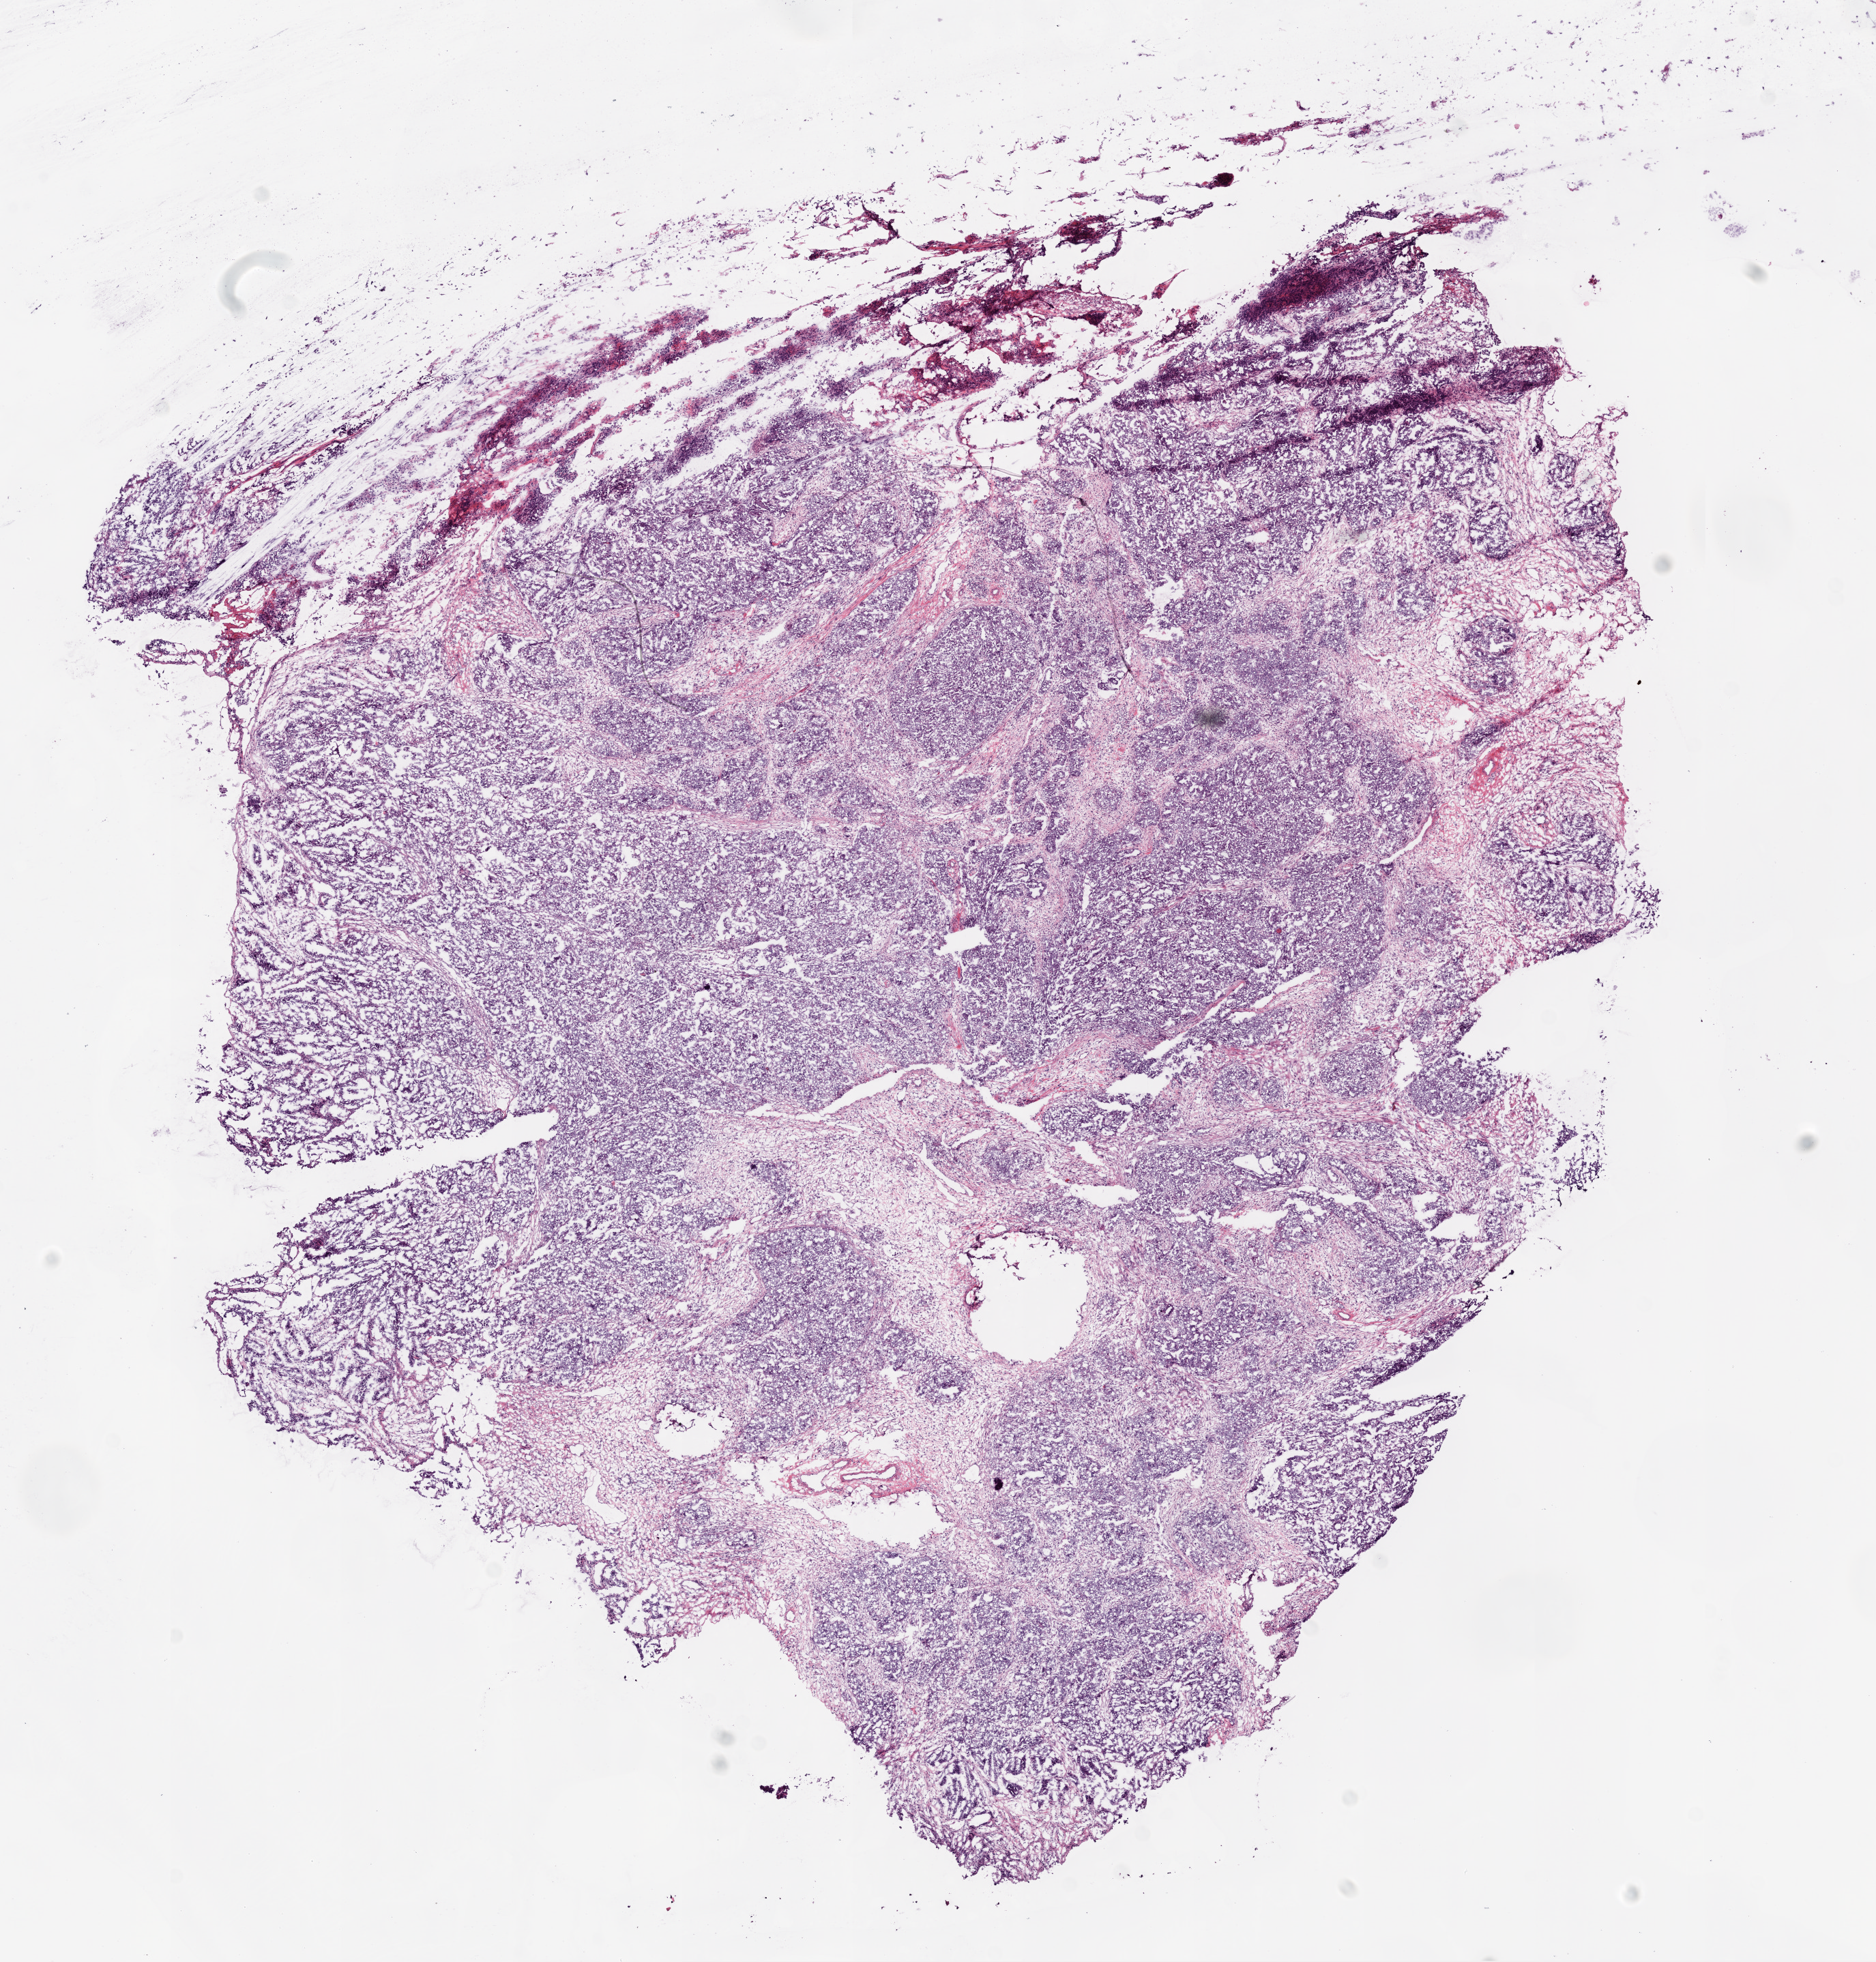
Whole-slide histology image, H&E, shown as a low-resolution overview of the whole scanned area (about 11.0 x 11.5 mm, slide scanned at 20x), frozen section from the bottom of the tissue portion, primary tumour sample from the ovary. Female, age 61 years at initial diagnosis. Histologic grade: G3 (poorly differentiated). Pathologist review of this section (percent, as recorded): tumour cells 90%, tumour nuclei 95%, normal cells 0%, stromal cells 10%, necrosis 0%.
Pathologic diagnosis: Serous cystadenocarcinoma, NOS. FIGO stage: IIIC.